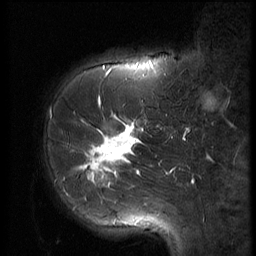
Breast MRI (dynamic contrast-enhanced), one sagittal slice. Slice 19 of 56 in the series (ordered by position). 3 images stored at this slice position (order not interpretable as contrast timing). 1.5 T. TE 4.2 ms, TR 9 ms. 2.5 mm slice thickness. 256 × 256 image matrix. Patient: female, 61 years. From the clinical record (not read from this slice): setting: breast cancer imaged before/during neoadjuvant chemotherapy; receptor status: HR-positive, HER2-negative.
Annotated regions visible in this slice (semi-automatic segmentation, software-assisted and operator-edited):
- analysis volume of interest (the breast-tissue region the enhancement analysis was run in; not a lesion): bounding box <47,89,153,191> (left, top, right, bottom; pixels)
- tumour enhancement mask (voxels above the 140 % enhancement threshold inside the analysis volume of interest): <78,115,143,188>